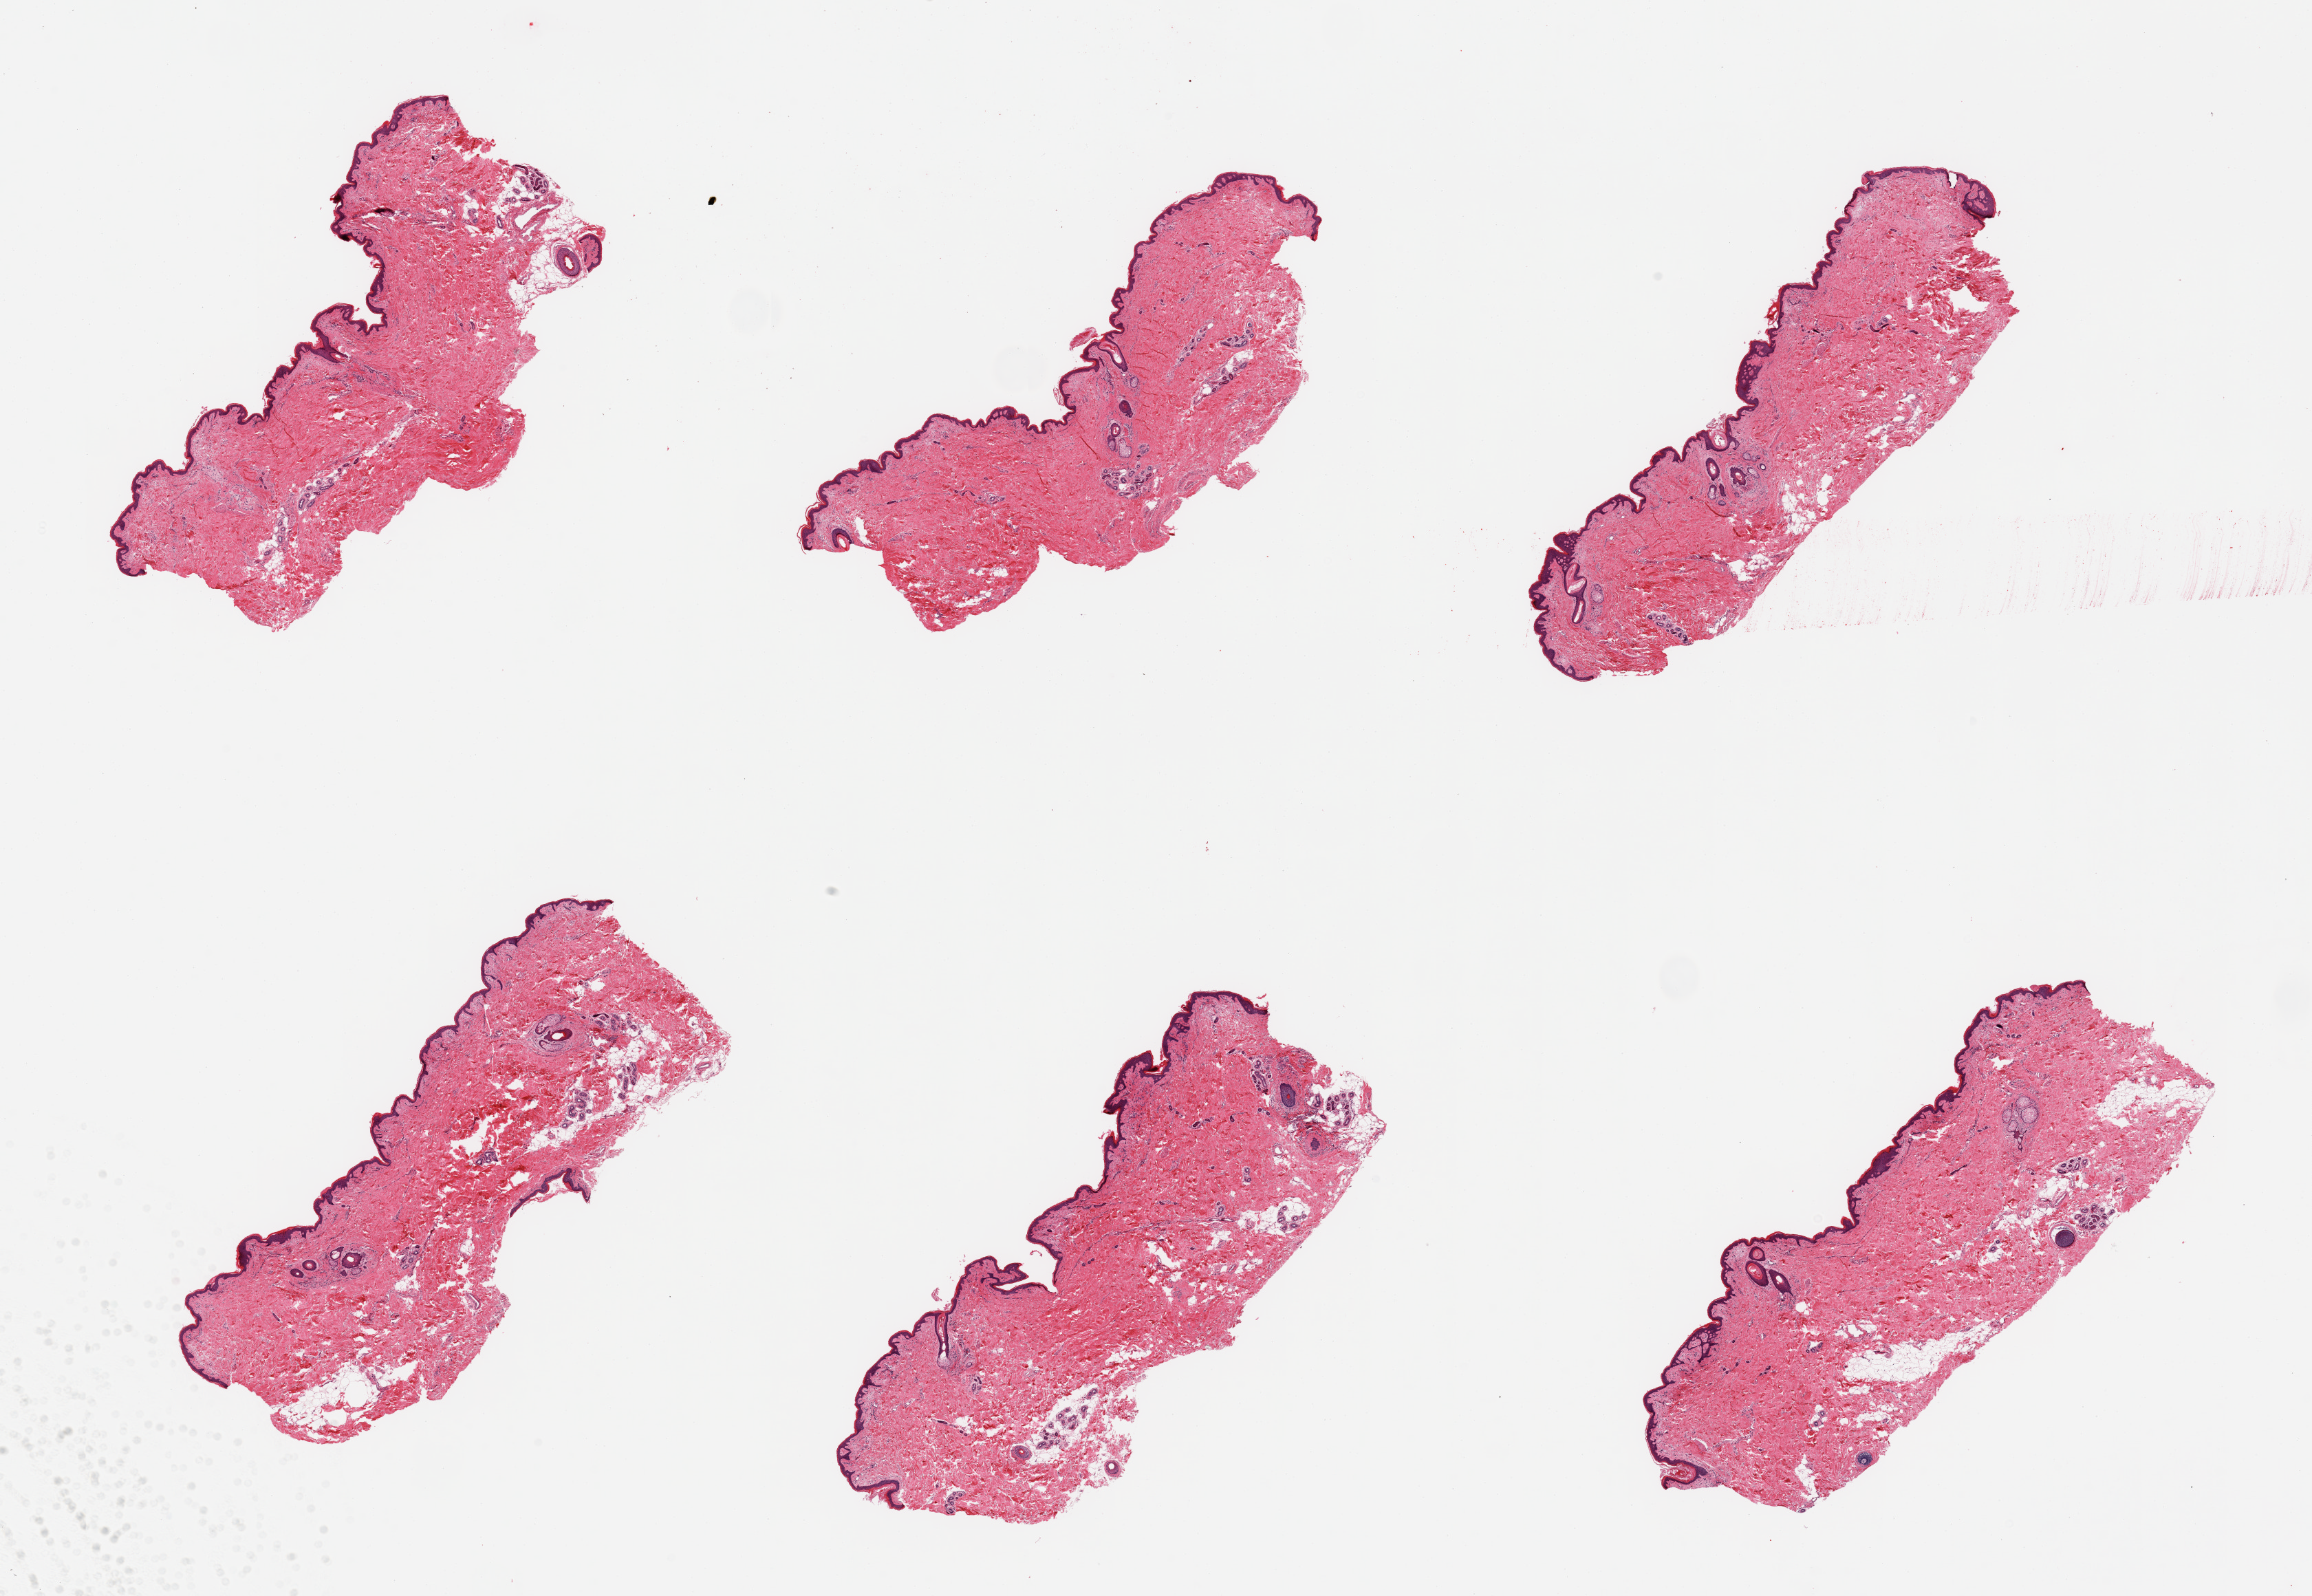
Digitized H&E-stained section, shown as a low-resolution overview of the whole scanned area (about 26.6 x 18.3 mm). PAXgene-fixed, paraffin-embedded tissue. Section of skin of suprapubic region (target tissue). Tissue donor sample.
- pathologist's review note for this sample: 6 pieces; well trimmed; 5-10% dermal fat